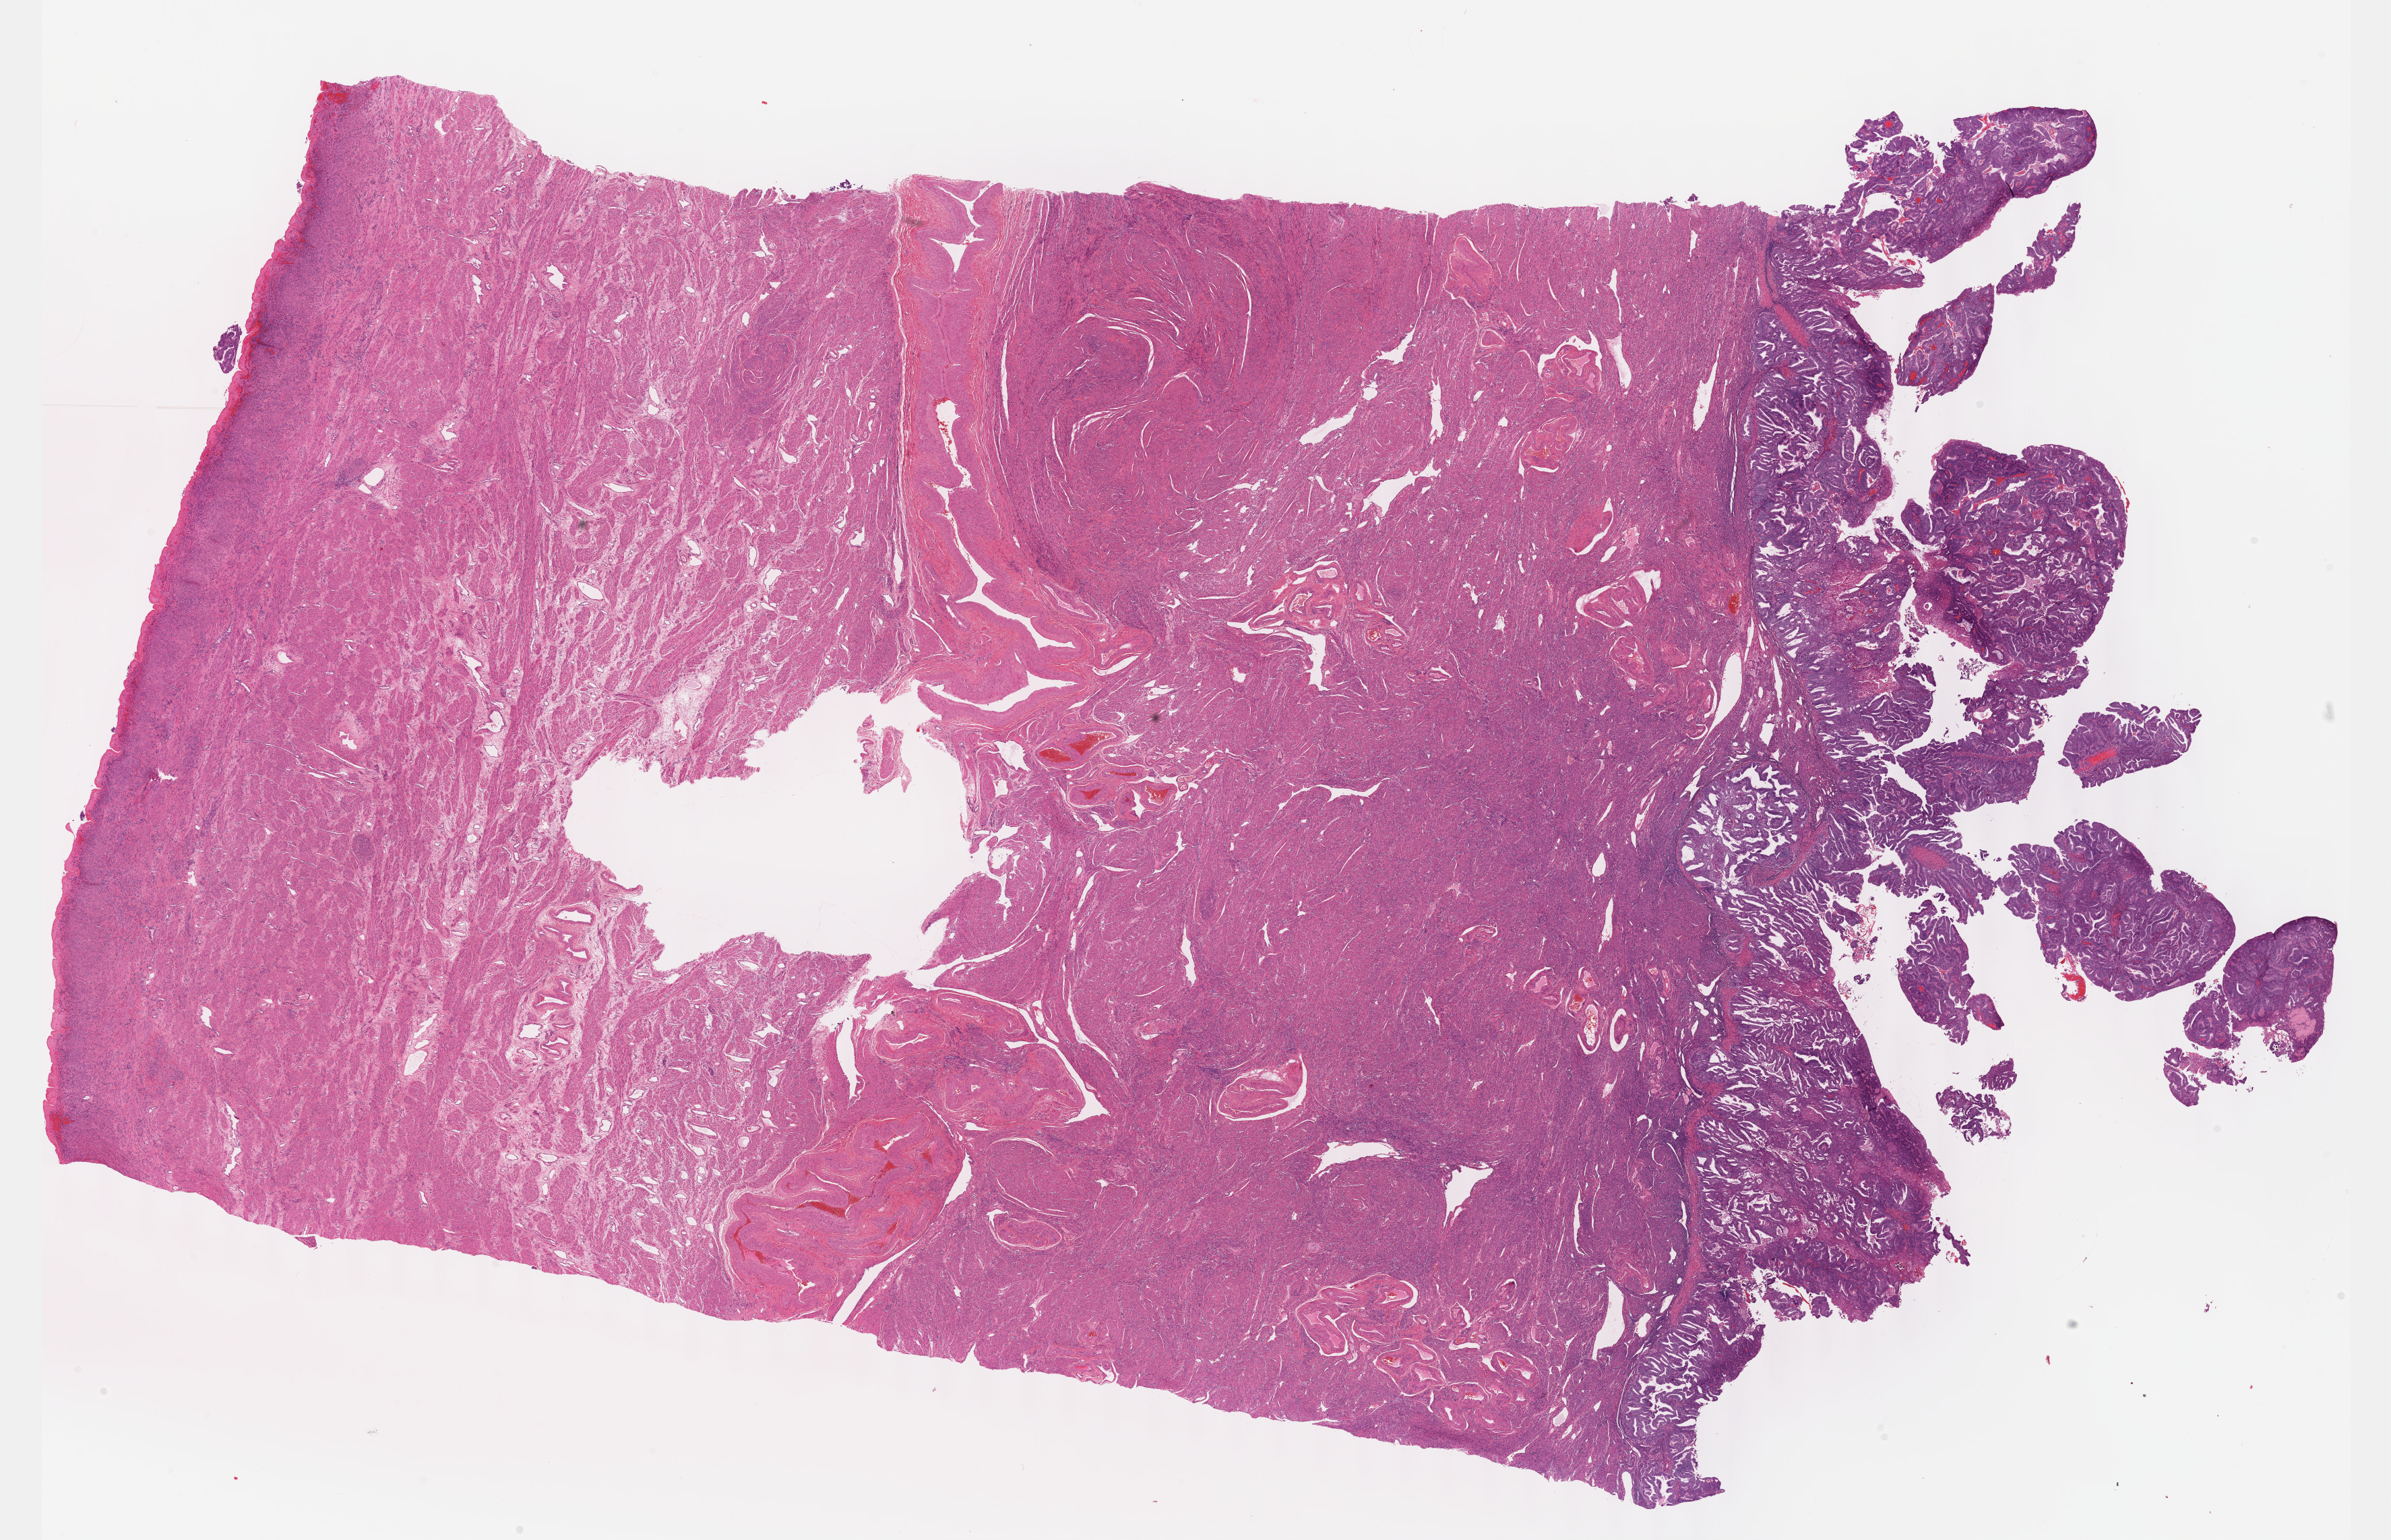
Whole-slide histology image, H&E, a low-resolution overview of the entire scanned area, about 28.7 x 18.5 mm (slide scanned at 40x), FFPE section, sample: primary tumour, uterus. Female, age 52 years at initial diagnosis. Histologic grade: G2 (moderately differentiated).
- FIGO stage: II
- diagnosis: Endometrioid adenocarcinoma, NOS